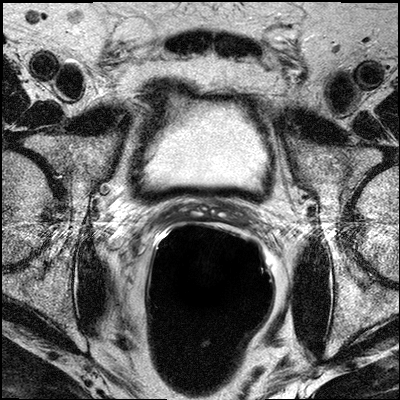
Prostate MRI examination; 3 images, each a single mid-volume slice chosen by position (not for content). Treatment context recorded for this patient: No surgery, Casodex, Leuprolide, RT.
Image 1: T2-weighted axial slice, series "T2W_TSE_AX", slice 17 of 32, 3 mm slice thickness.
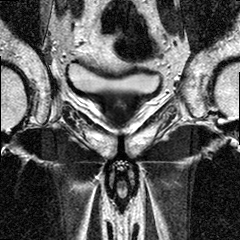
Image 2: coronal T2-weighted image, series "T2W_TSE_COR", slice 13 of 24, 3 mm slice thickness.
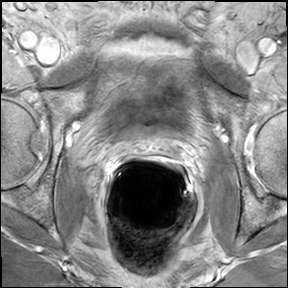
Image 3: axial dynamic contrast-enhanced (DCE) T1-weighted image, series "AX BLISS_GAD_8", slice 15 of 28, dynamic phase 5 of 8.
MRI report (verbatim):
The zonal anatomy is preserved. The prostate measures in its maximal transverse diameter of 4.5 in its maximal AP diameter 2.3 and max. CC diameter 3.3 cm. The estimated gland volume is 18 cc. In the mid 3rd of the prostate in the left posterior lateral peripheral zone between 3 and 5 o'clock there is a T2 hypointense geographic area measuring 13 x 13 mm which shows suspicious enhancement in the dynamic series; this should be considered as the dominant nodule. In this location (4-5 o'clock) there is a irregular capsule seen, yet no tumor masses beyond the capsule. The findings are suggestive for capsular infiltration, without manifest extracapsular disease. The left neurovascular bundle is free. There are several smaller suspicious area, also in the right prostate suggestive for focal multifocal disease. The right neurovascular bundle is free; there is no seminal vesicle infiltration. There is no pelvic lymphadenopathy (no enlarged lymph nodes in the obturator and iliac stations). There is 1 very well circumscribed triangular-shaped sclerosing bone lesion in the iliac in the right iliac bone, unlikely related to prostatic disease. IMPRESSION: Likely bilateral prostate cancer with dominant nodule in the left posterior lateral peripheral zone, mid 3rd of the prostate, between 3 and 5 o'clock. In this location. findings are suggestive for capsular infiltration, however no evidence of manifest extracapsular disease (on either side). Both neurovascular bundles are uninvolved. No seminal vesicle infiltration. No pelvic lymphadenopathy.

Prostate biopsy pathology (as recorded):
The specimen consists of multiple brown/tan core biopsies measuring in length from 0.2 cm to 2.3 cm and 0.1 cm in diameter each. The specimen is submitted in toto in six cassettes as follows: 1 right PZ, 2 right PZ/TZ, 3 right apex, 4 left PZ, 5 left PZ/TZ, AND 6 left apex.PROSTATE BIOPSIES: 1. RIGHT PZ: PROSTATIC ADENOCARCINOMA, GLEASON SCORE 3+3=6/10, INVOLVING <5% (ONE CORE) OF TISSUE REPRESENTED. 2. RIGHT PZ/TZ: BENIGN PROSTATIC TISSUE. NO TUMOR IDENTIFIED. 3. RIGHT APEX: BENIGN PROSTATIC TISSUE. NO TUMOR IDENTIFIED. 4. LEFT PZ: PROSTATIC ADENOCARCINOMA, GLEASON SCORE 3+4=7/10, INVOLVING 40% (TWO CORES) OF TISSUE REPRESENTED. 5. LEFT PZ/TZ: PROSTATIC ADENOCARCINOMA, GLEASON SCORE 3+3=6/10, INVOLVING 30% (TWO CORES) OF TISSUE REPRESENTED. PERINEURAL INVASION NOTED. 6. LEFT APEX: PROSTATIC ADENOCARCINOMA, GLEASON SCORE 3+4=7/10, INVOLVING 80% (TWO CORES) OF TISSUE REPRESENTED. PERINEURAL INVASION NOTED.